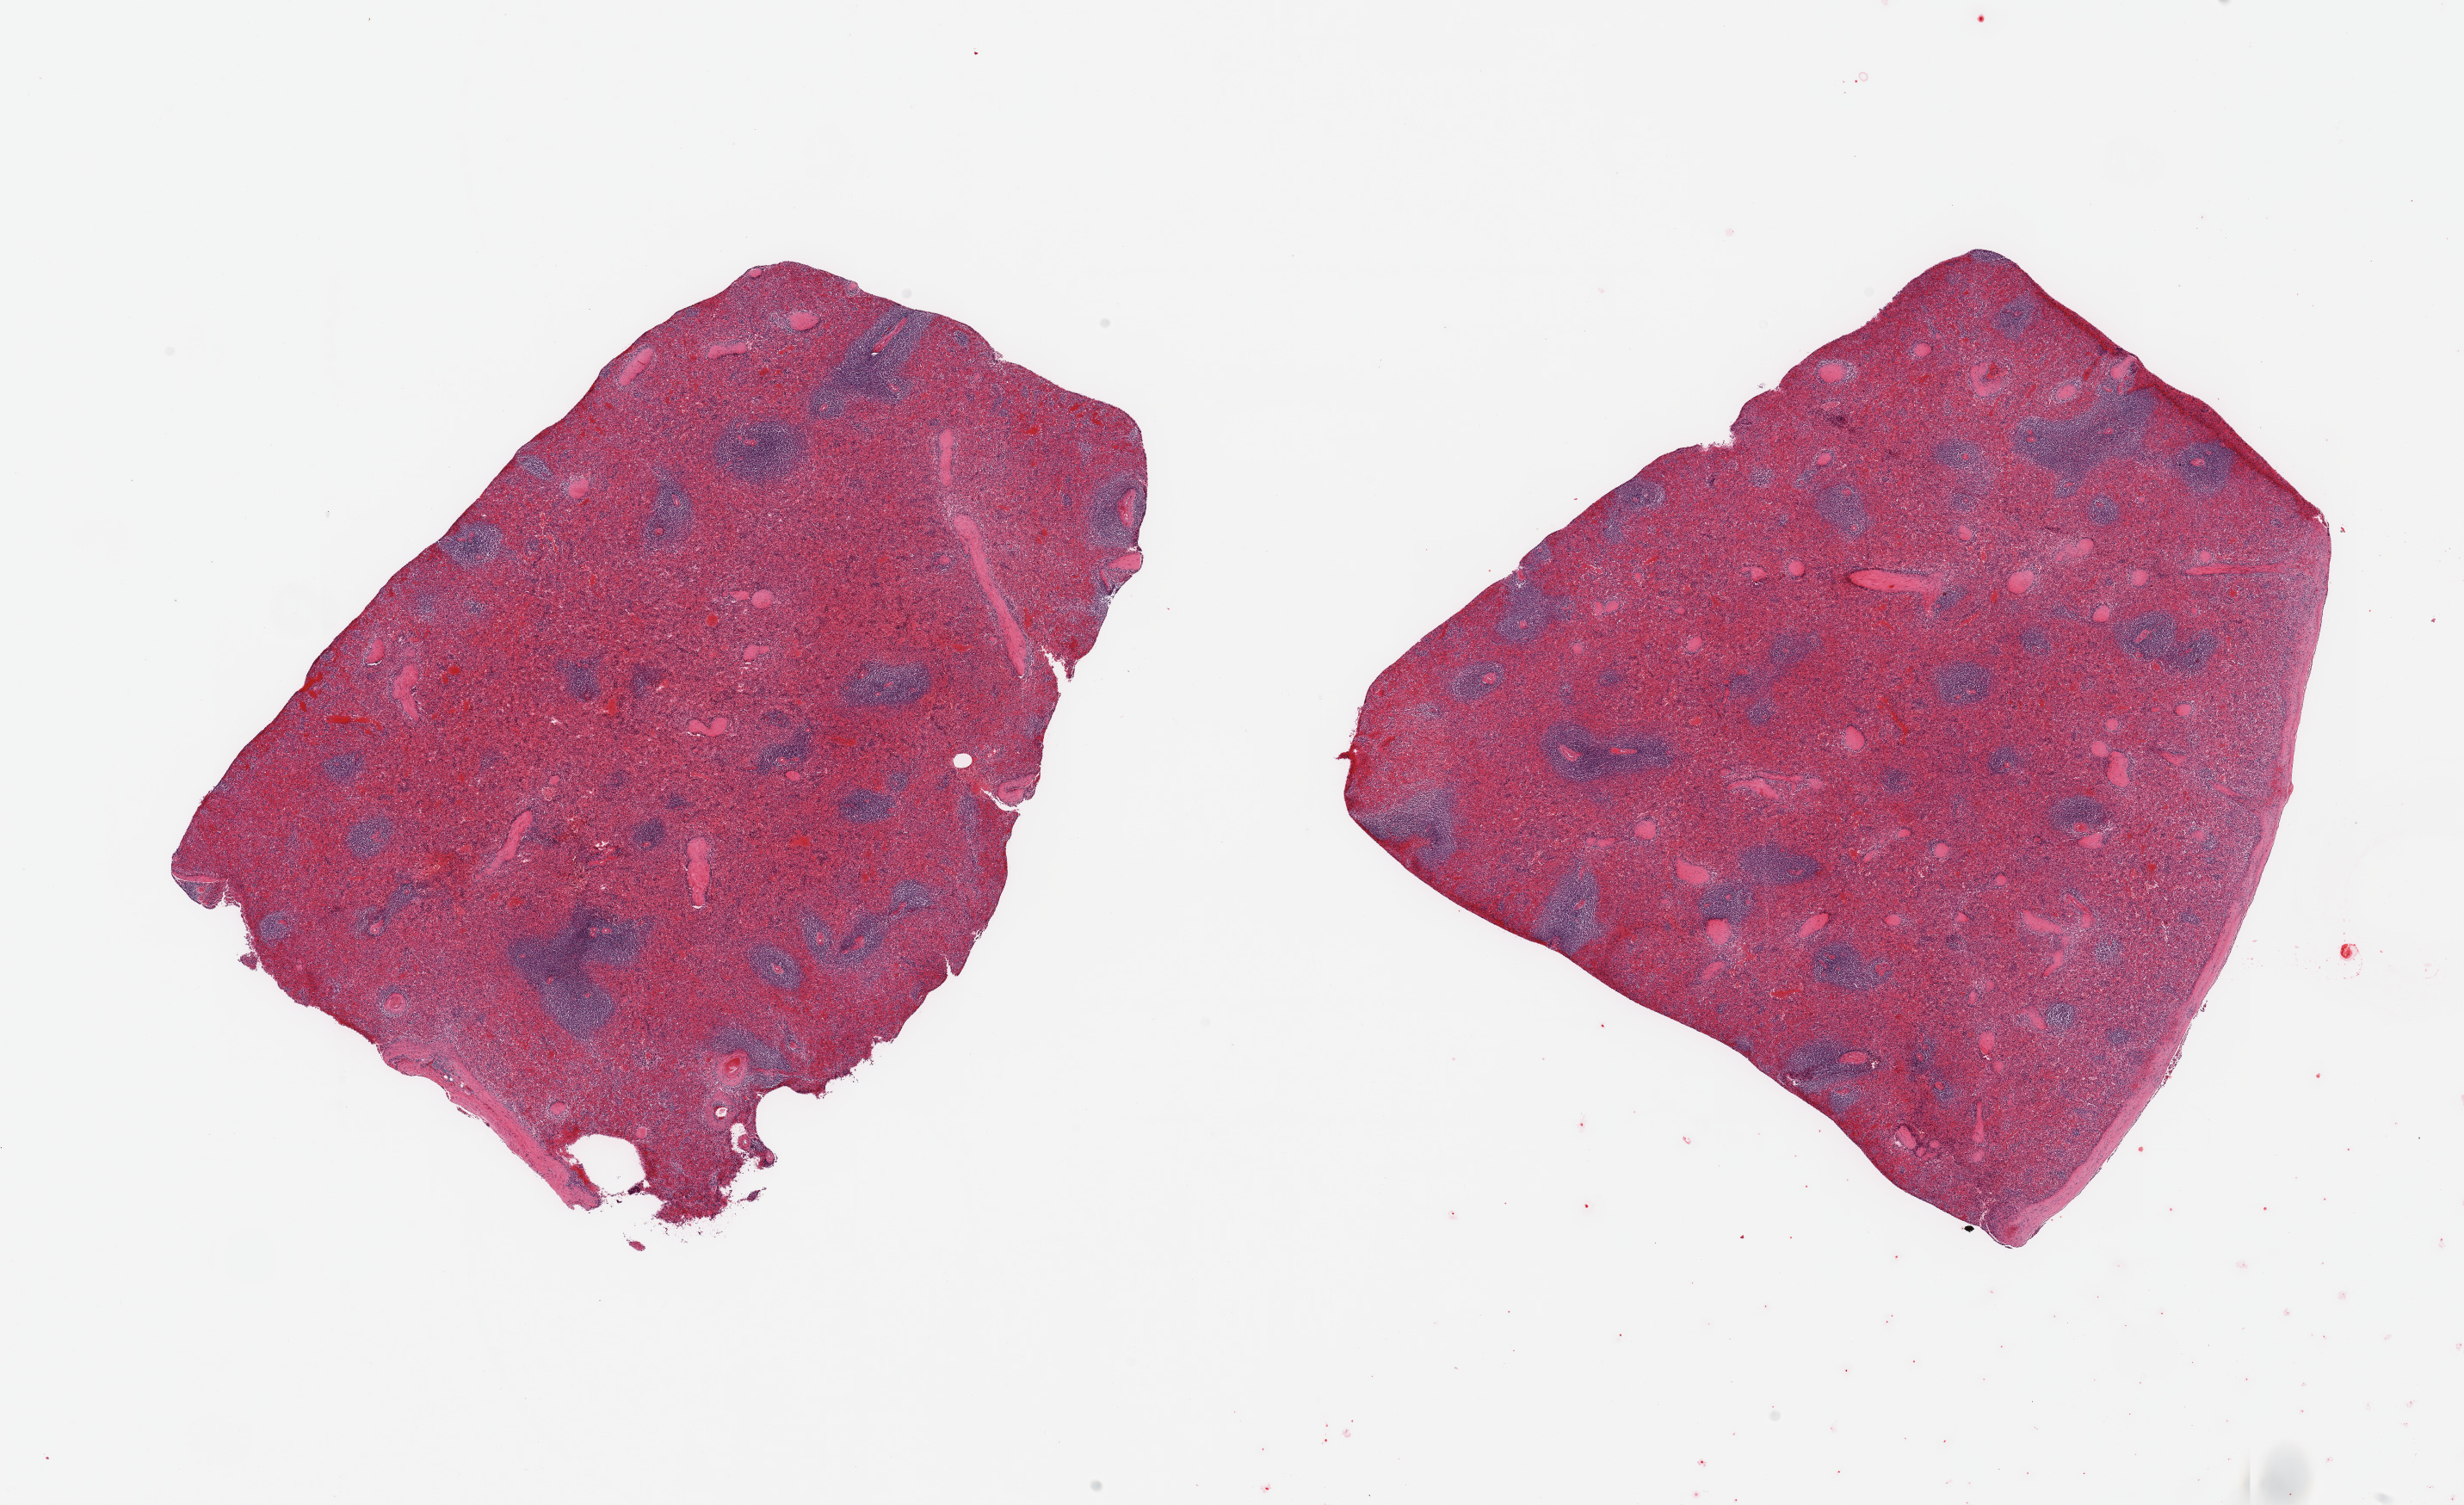
Hematoxylin and eosin (H&E) whole-slide image, shown as a low-resolution overview of the whole scanned area (about 22.6 x 13.8 mm), PAXgene-fixed, paraffin-embedded tissue, sampled site (target tissue): spleen, tissue donor sample. Male donor.
Review note (as recorded): 2 pieces; marked congestion, capsule is present (target is 5mm below).